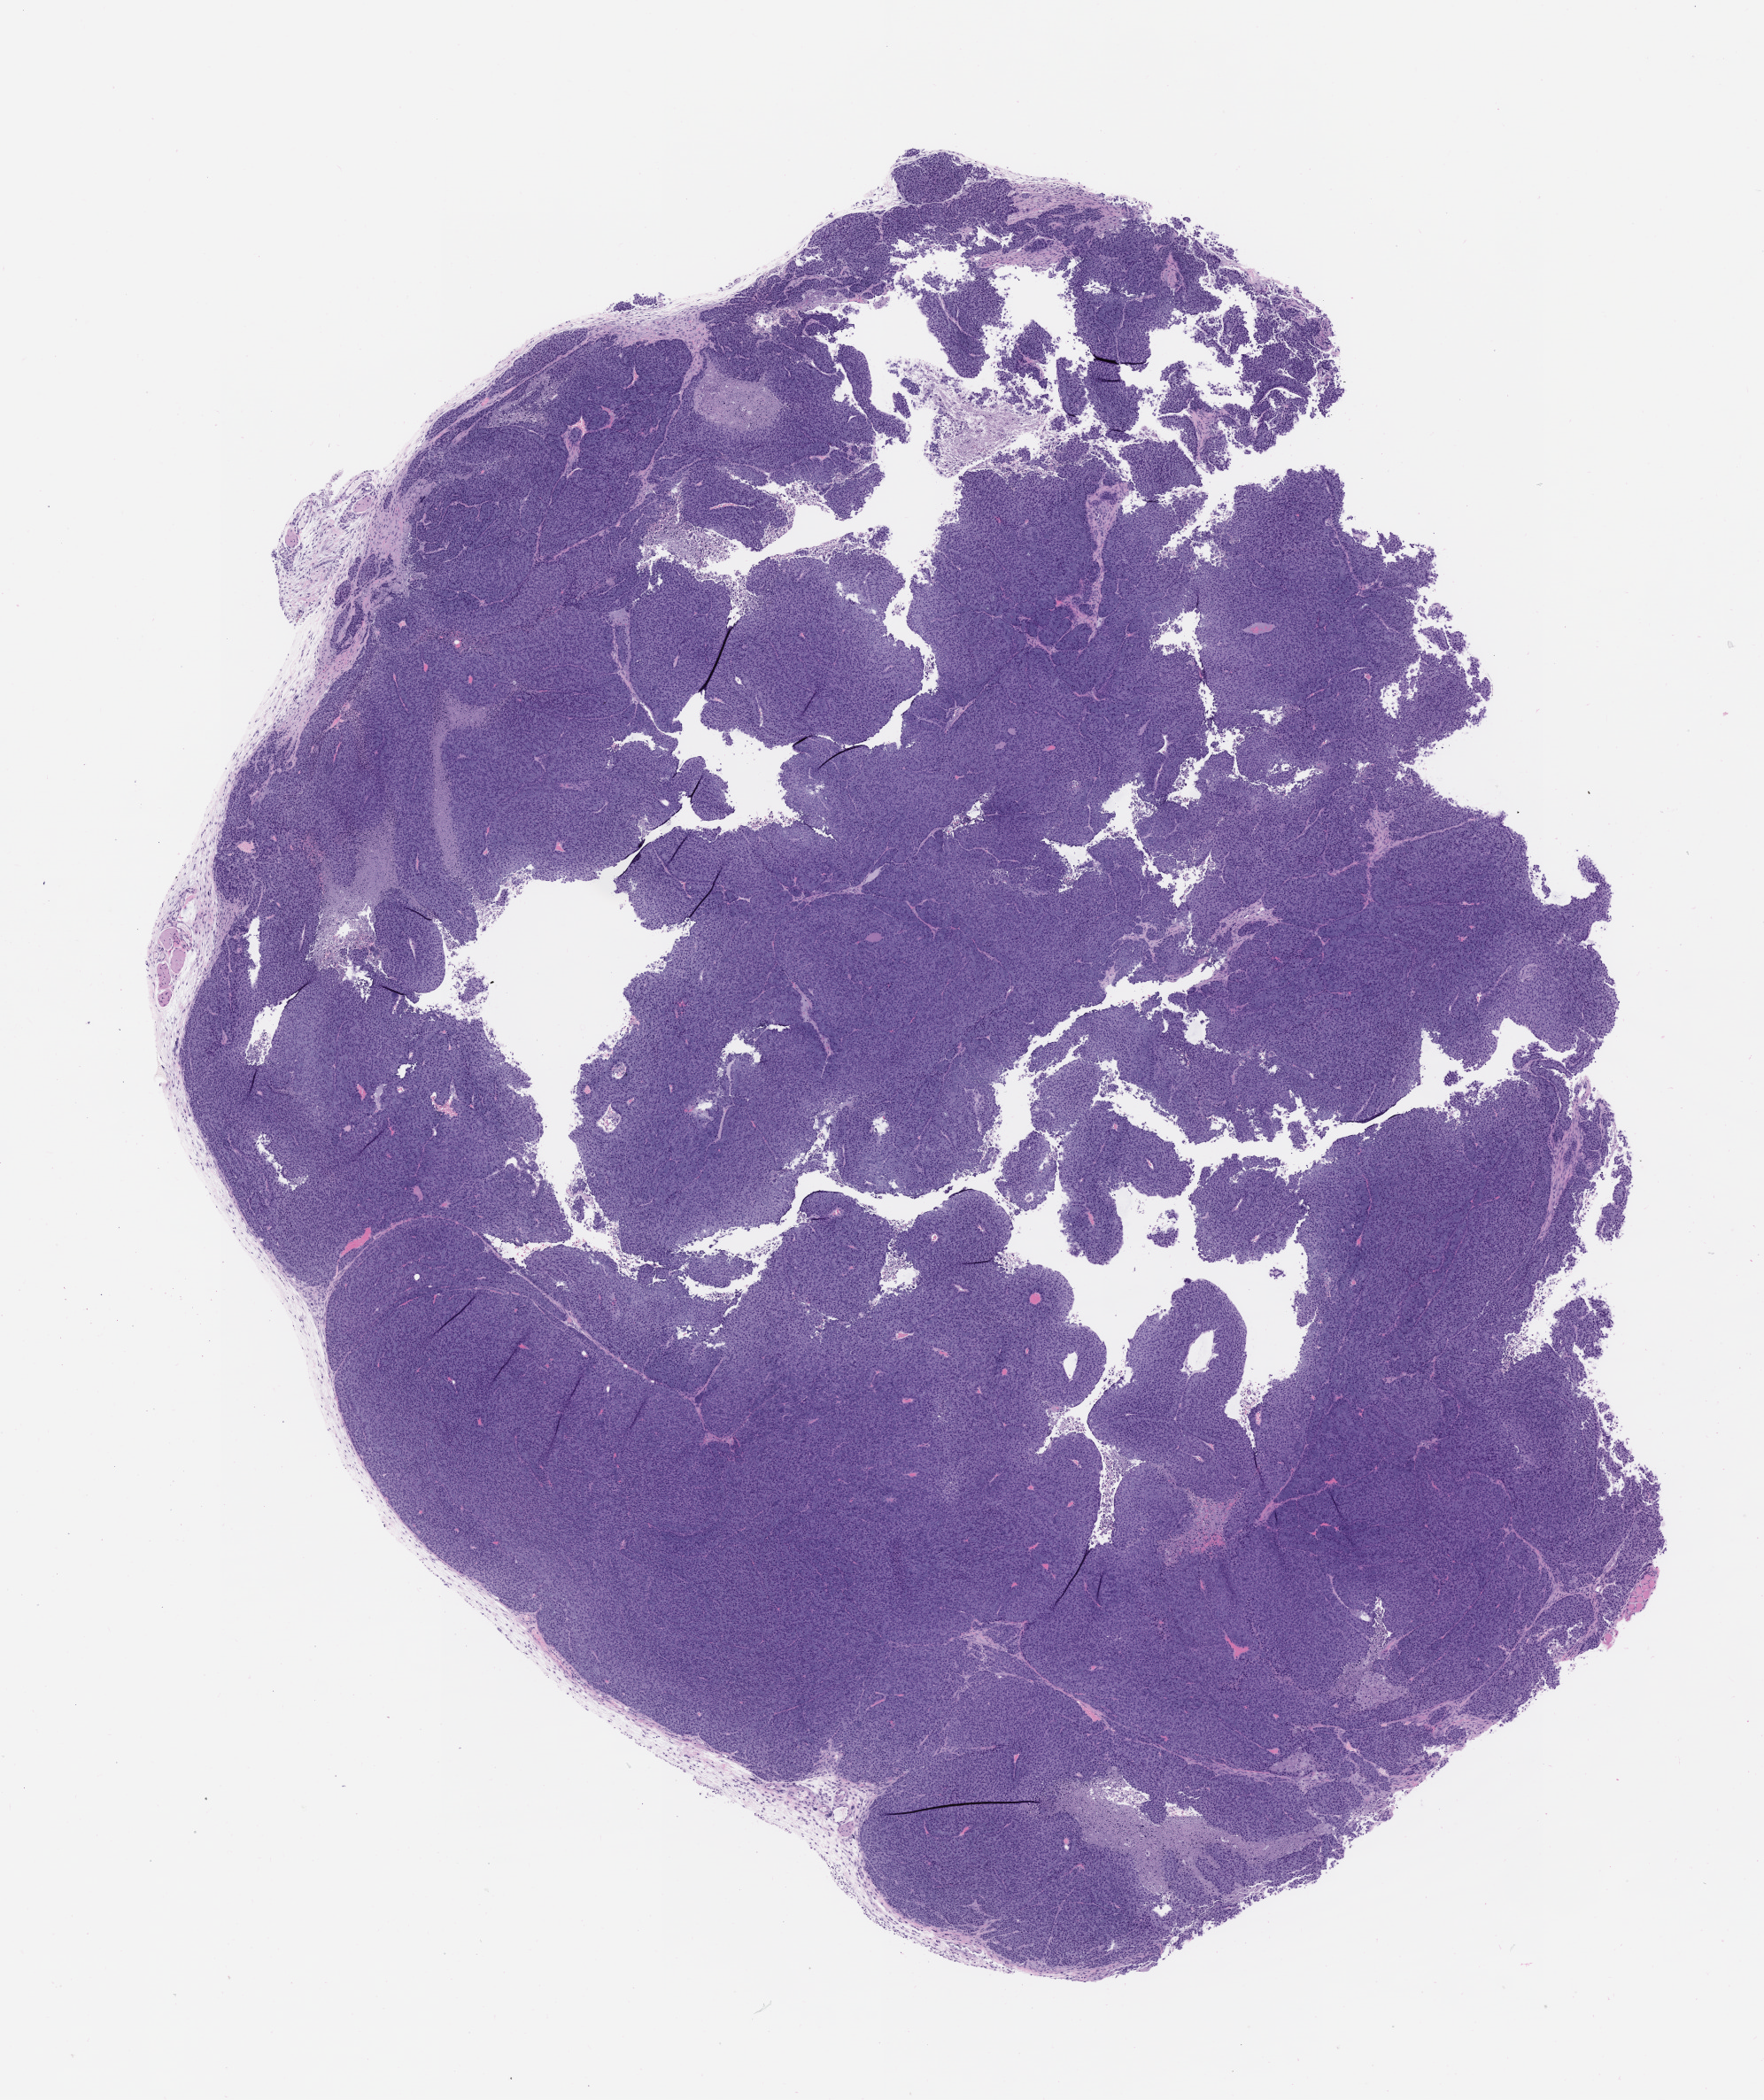
Hematoxylin and eosin (H&E) whole-slide image of a patient-derived xenograft (PDX) tumor grown in a mouse, passage 2, shown as a low-resolution overview of the whole scanned area (about 8.0 x 9.5 mm), formalin-fixed, paraffin-embedded (FFPE) tissue, originating tumor site category: head and neck.
* originating patient diagnosis: Acinar Cell Carcinoma